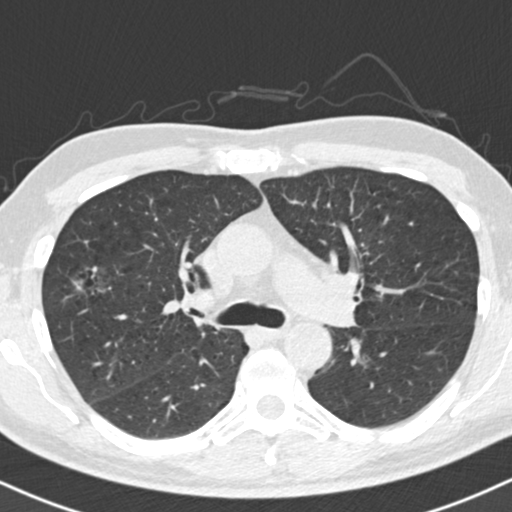
Low-dose screening chest CT, axial slice. Baseline annual screen. Lung window (W 1500 / L -600 HU). 2 mm slice thickness. 512 × 512 image matrix. Male participant, aged 56 years at enrolment. Former smoker at enrolment.
• Expert reader's lesion annotation, bounding box (x1, y1, x2, y2) in pixels: (47, 254, 137, 319).
• Screening reader's record for this exam: no non-calcified nodule ≥4 mm recorded.
• Lung cancer was diagnosed 392 days after this screen (after the second annual screen): bronchiolo-alveolar adenocarcinoma, NOS, right upper lobe, well differentiated (G1), stage IIB (AJCC 6th edition), 30 mm at pathology.